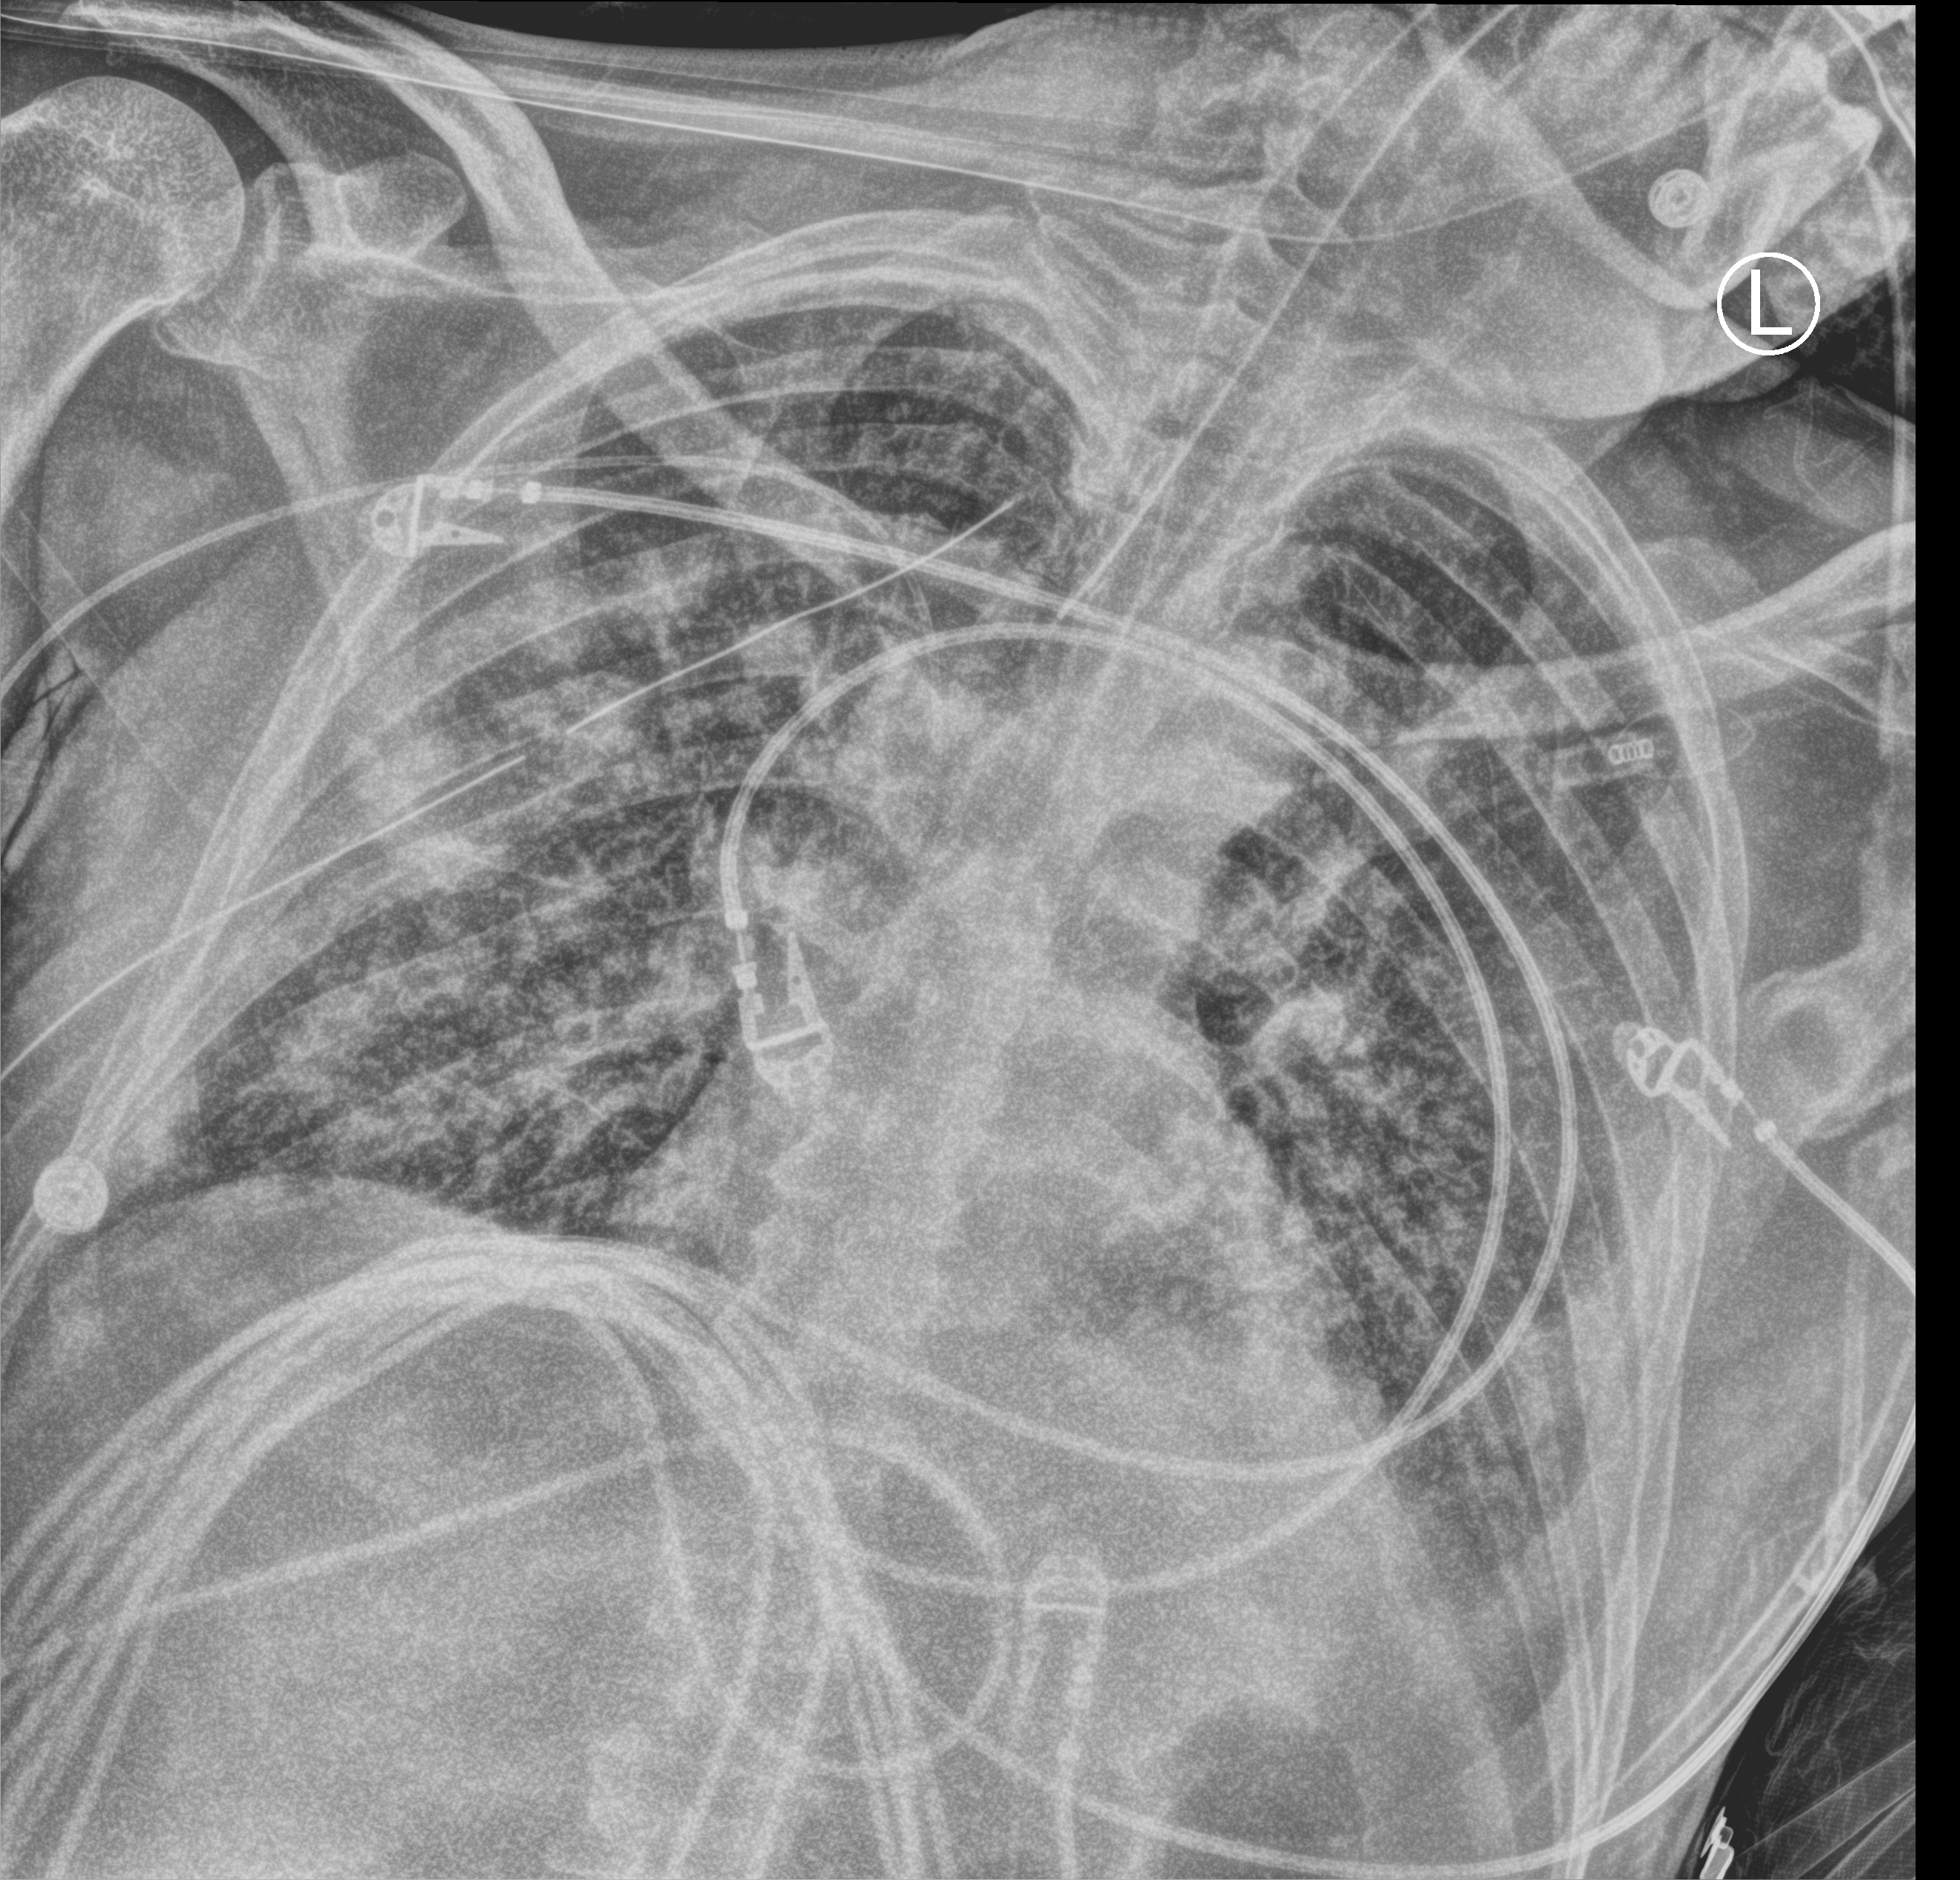
Portable chest radiograph; anteroposterior (AP) projection. Patient hospitalised with COVID-19; male, aged 18–59 years.
Admission-level facts for this patient (not findings on this image; timing relative to this image not recorded):
- mechanically ventilated during this hospital stay: yes
- admitted to intensive care during this hospital stay: yes